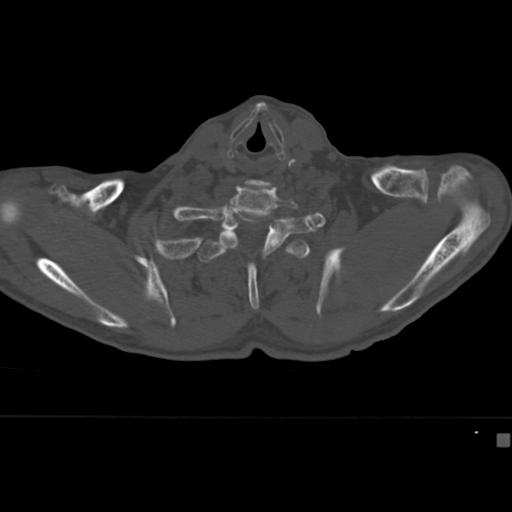
CT including the spine, one axial slice. Position 350 of 430 along the scan axis. Bone window (W 1800 / L 400 HU). 512 × 512 image matrix, field of view 337 × 337 mm. Male patient, age 64 years. From the clinical record (not read from this slice): primary cancer: uterus.
Annotated regions visible in this slice (semi-automatically segmented with operator editing):
- T2 vertebra: box from (x=198, y=236) to (x=311, y=310) px